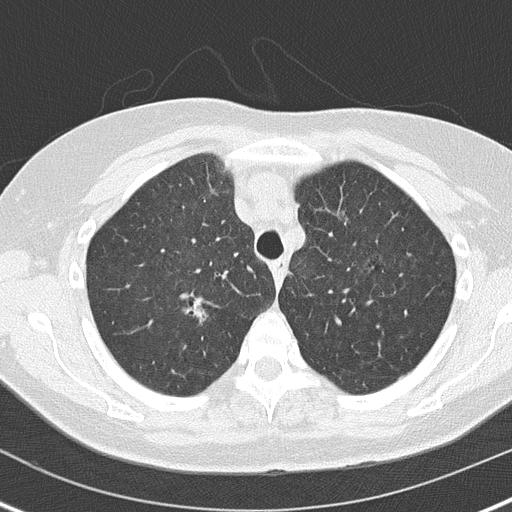
Axial slice from a low-dose chest CT screening exam; baseline screening round; lung window (W 1500 / L -600 HU); lung (sharp) reconstruction kernel (B50f); slice 39 of 162 in the series; 512 × 512 image matrix. Female participant, aged 61 years at enrolment. Current smoker at enrolment.
Lesion marked by an expert reader, bounding box (x1, y1, x2, y2) in pixels: (178, 289, 220, 327). Screening reader's record for this exam (one nodule recorded; not confirmed to be the boxed lesion): non-calcified nodule or mass ≥4 mm, right upper lobe, 8 × 5 mm, smooth margins, soft tissue attenuation.